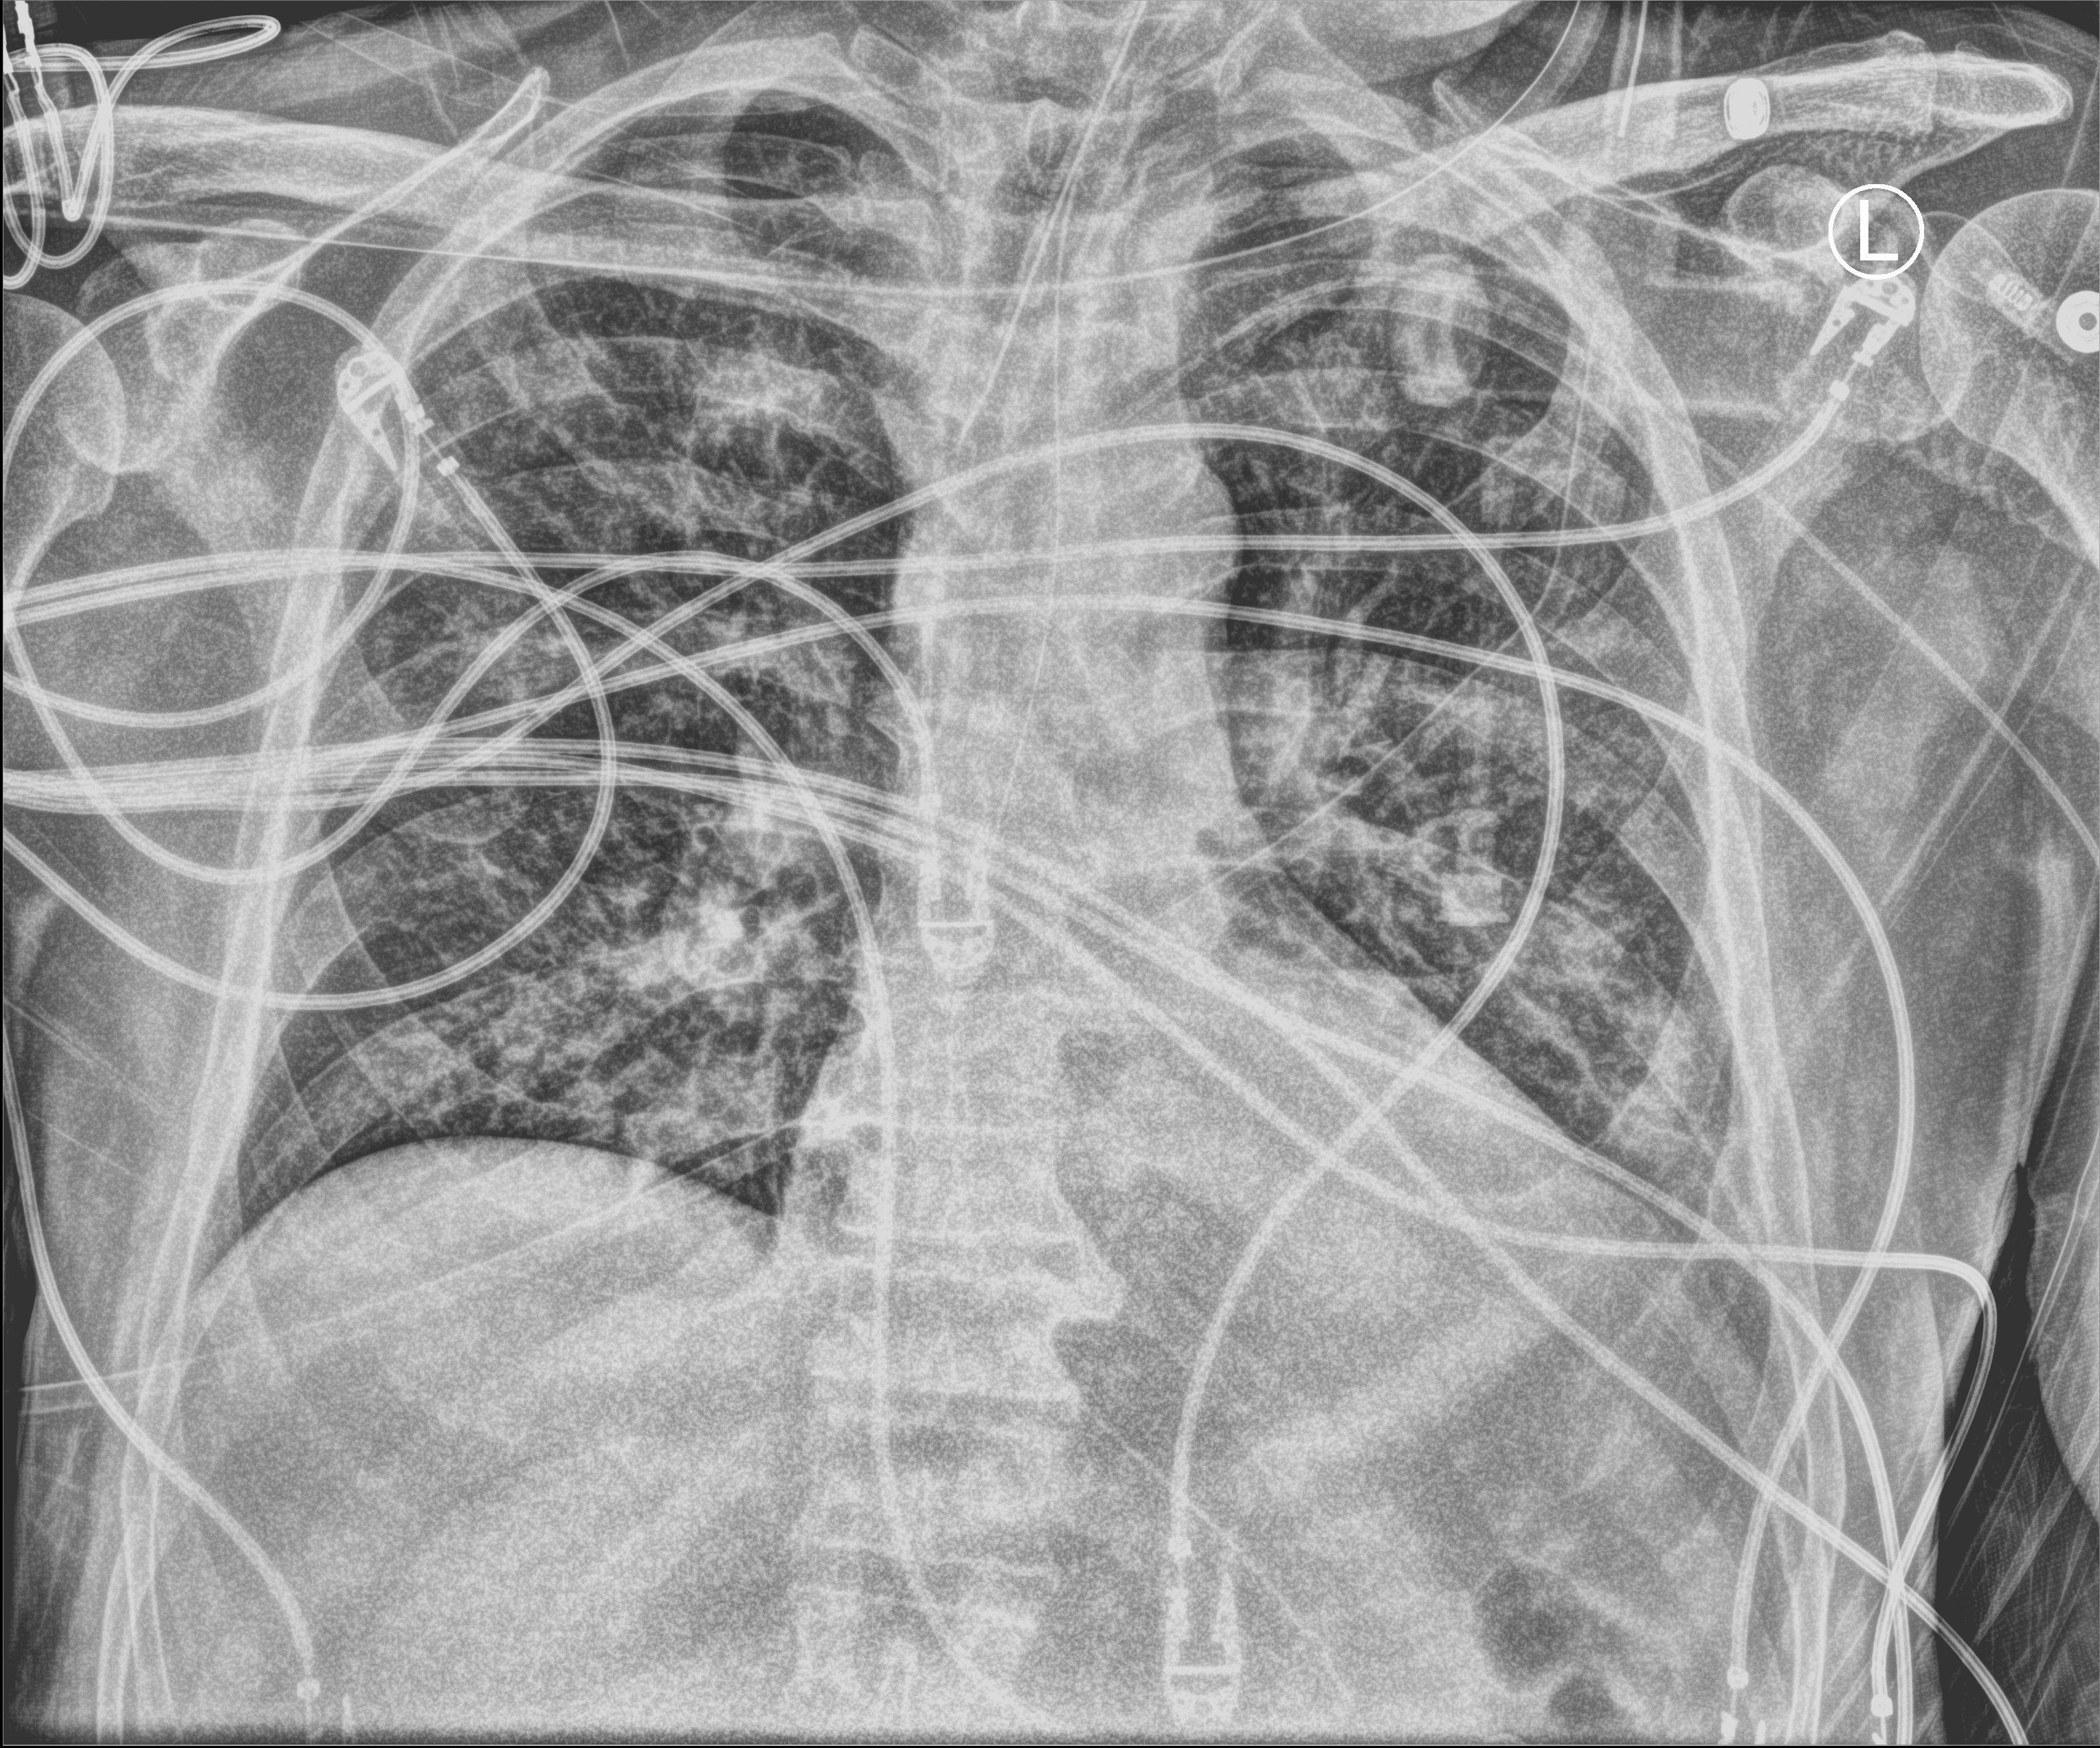
Bedside chest radiograph (computed radiography). Male patient hospitalised with COVID-19, age 60–74 years.
From the hospital-stay record, not from the radiograph (when in the stay this image was taken is not recorded): mechanically ventilated during this hospital stay: yes.